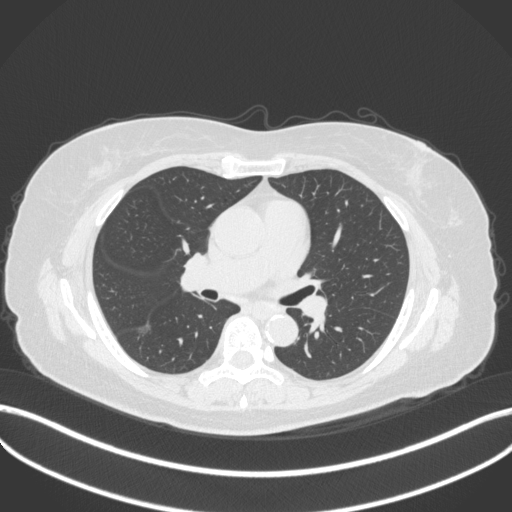
Chest CT, one axial slice. Position 180 of 322 along the scan axis. Lung window (W 1500 / L -600 HU). 1 mm slice thickness. 512 × 512 image matrix. Patient: female, 64 years. Case-level facts recorded for this patient, not image findings: clinical TNM (as recorded): T1c N0 M0.
Outlined on this slice (bounding box drawn by a radiologist):
- lung tumour (recorded histology: adenocarcinoma): bounding box (x1, y1, x2, y2) in pixels: (134, 319, 154, 337)